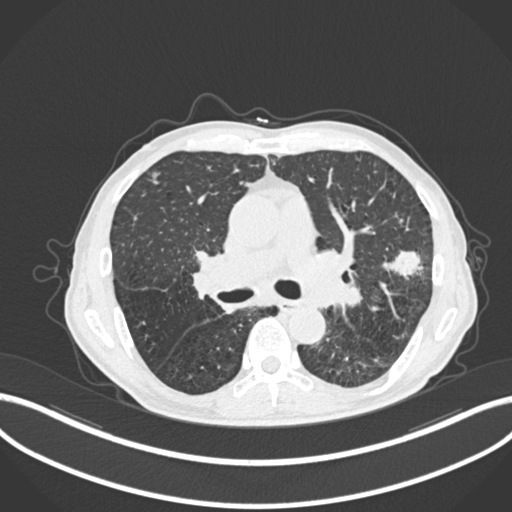
Chest CT, one axial slice; position 147 of 287 along the scan axis; 120 kVp; lung window (W 1500 / L -600 HU); 512 × 512 image matrix, field of view 400 × 400 mm. Patient: male, 74 years. Case-level facts recorded for this patient, not image findings: clinical TNM (as recorded): T2a N1 M0.
Outlined on this slice (rectangle marked by the reading radiologist):
- lung tumour (recorded histology: adenocarcinoma): bounding box <380,241,427,280> (left, top, right, bottom; pixels)